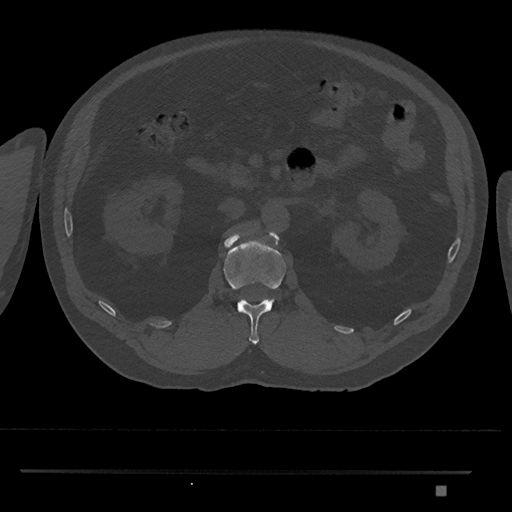
CT including the spine, one axial slice; slice 810 of 1134 in the series (ordered by position); 120 kVp; bone window (W 1800 / L 400 HU); 0.5 mm slice thickness; 512 × 512 image matrix, field of view 429 × 429 mm. Patient: male, 65 years. From the clinical record (not read from this slice): primary cancer: prostate.
Annotated regions visible in this slice (semi-automatic segmentation, software-assisted and operator-edited):
- L1 vertebra: box from (x=223, y=230) to (x=287, y=344) px